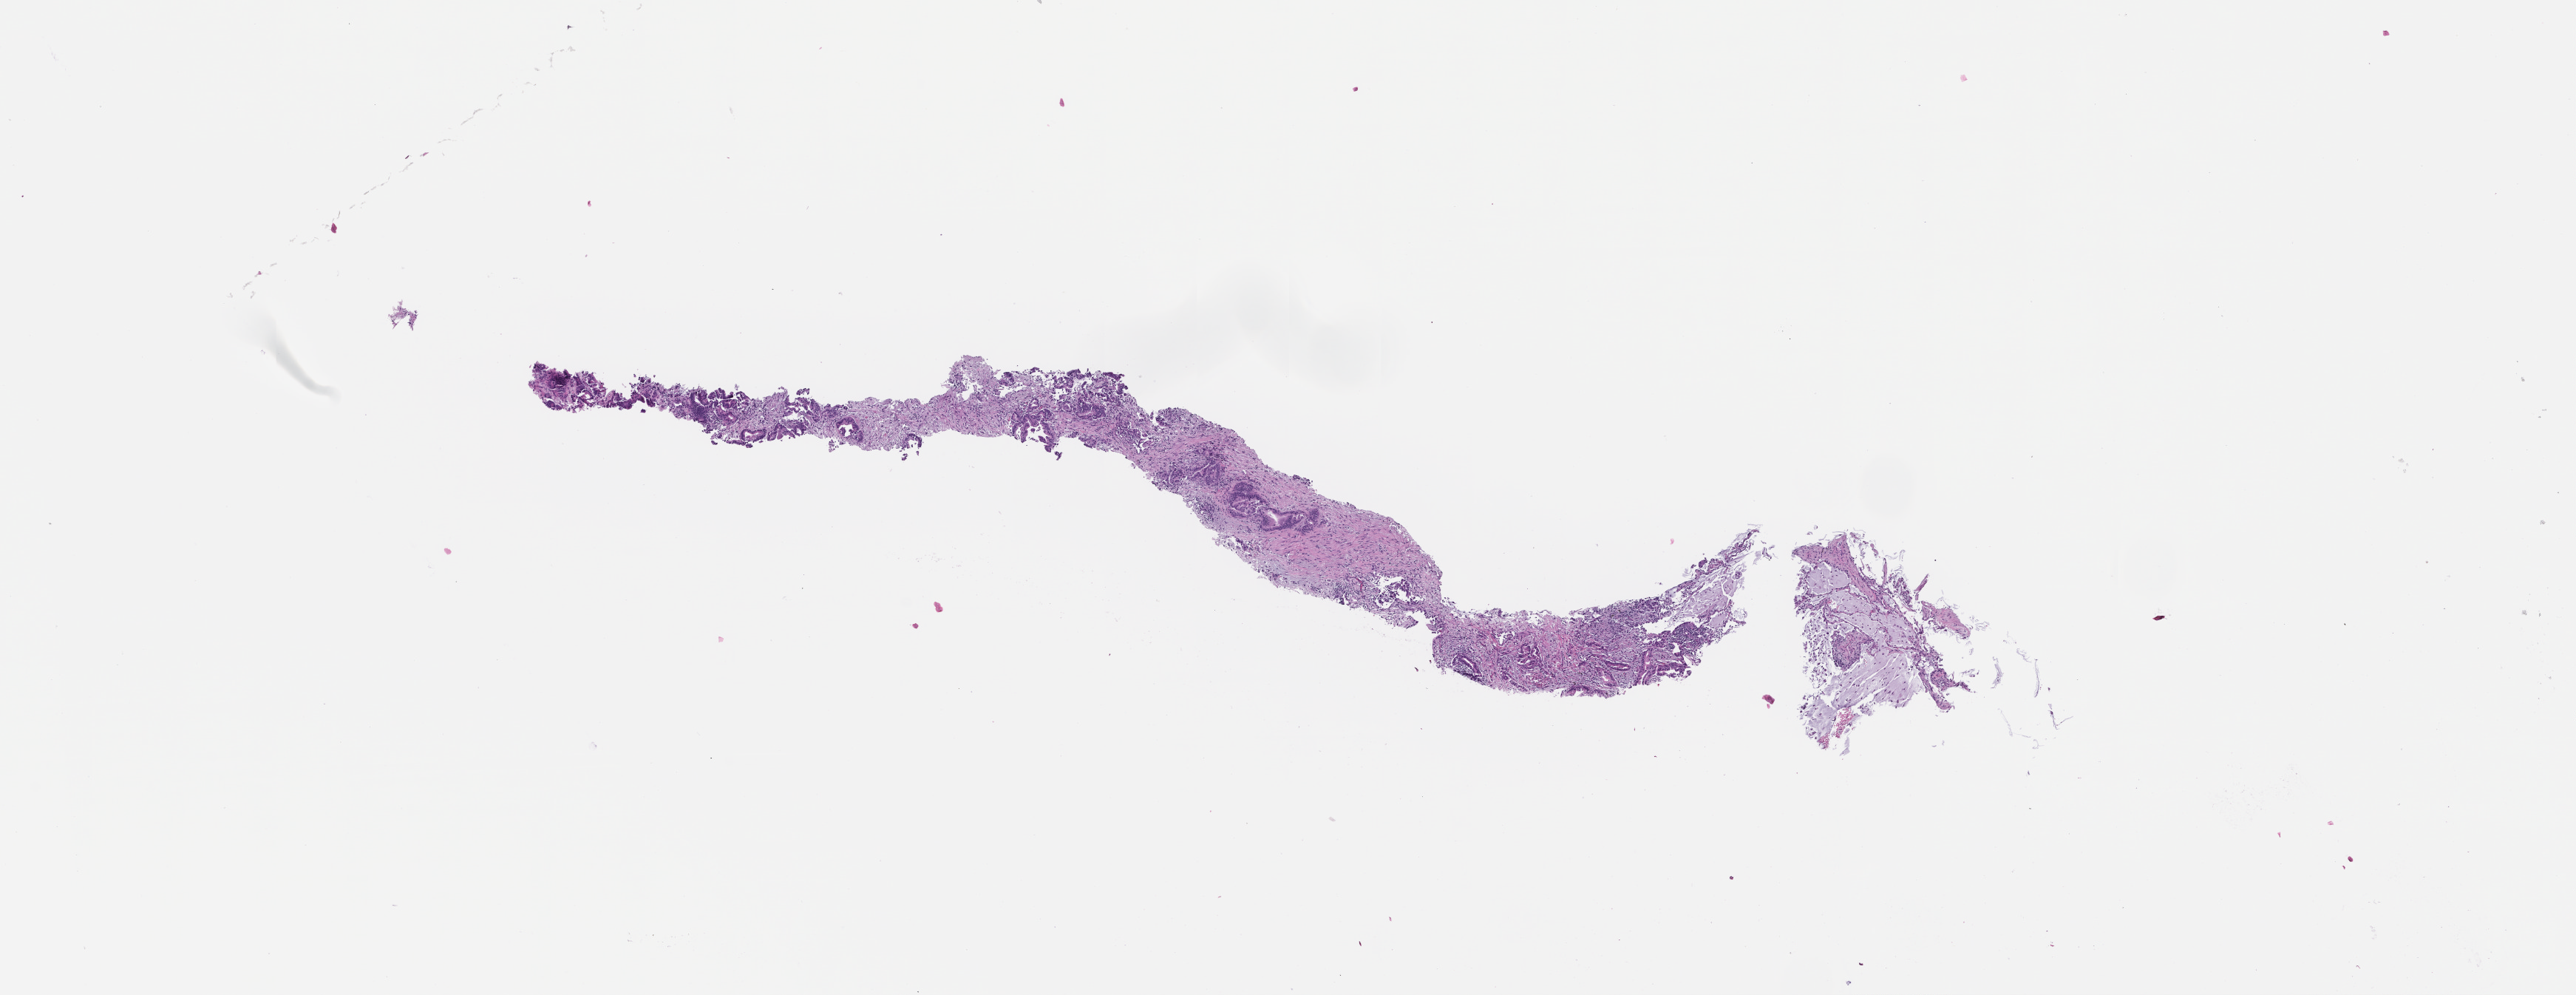
Whole-slide image, H&E stain, low-resolution overview of the scanned area, about 14.1 x 5.4 mm; formalin-fixed, paraffin-embedded (FFPE) tissue; tissue site: lung; specimen time point: archival tissue. Patient: female.
This section: primary tumour tissue. Diagnosis: Non-Small Cell Lung Carcinoma.